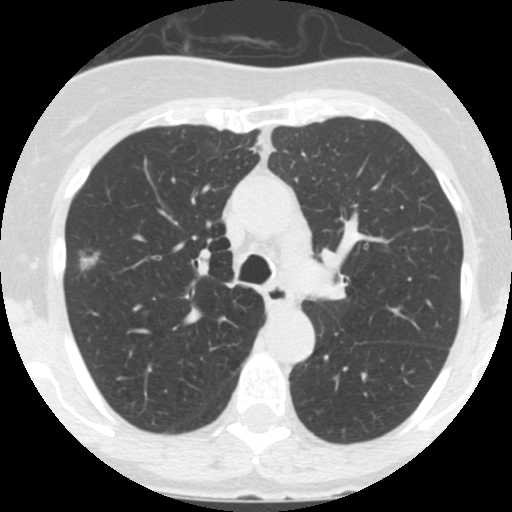
Low-dose screening chest CT, one axial slice. Slice 98 of 146 in the series (ordered by position). 120 kVp. Lung window (W 1500 / L -600 HU). 2.5 mm slice thickness. 512 × 512 image matrix, field of view 280 × 280 mm.
Outlined on this slice (manually delineated by an expert):
- lesion 1 (tumor, upper lobe of right lung): bounding box <78,248,99,270> (left, top, right, bottom; pixels)